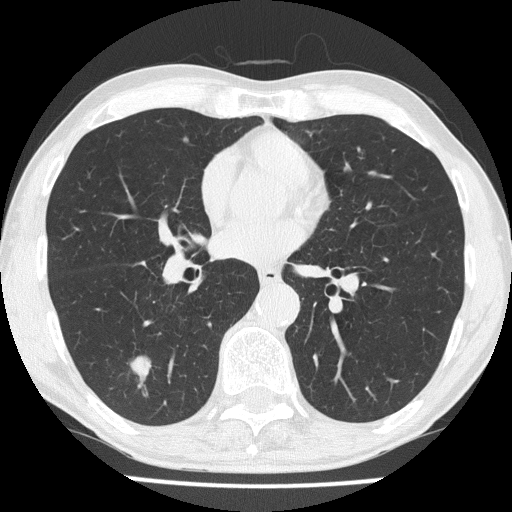
Axial slice from a low-dose chest CT screening exam. Third annual screen. Lung window (W 1500 / L -600 HU). 2 mm slice thickness. Lung (sharp) reconstruction kernel (FC51). Male, age 59 years at enrolment. Former smoker at enrolment.
Expert reader's lesion annotation, box from (x=111, y=346) to (x=160, y=393) px. Screening reader's record for this exam (one nodule recorded; not confirmed to be the boxed lesion): non-calcified nodule or mass ≥4 mm, right lower lobe, 20 × 16 mm, smooth margins, soft tissue attenuation, pre-existing on the prior screen: no. Official screen result: positive, other. Later outcome: lung cancer diagnosed 25 days after this screen — small cell carcinoma, NOS, right lower lobe, stage IIA (AJCC 6th edition), 20 mm at pathology.